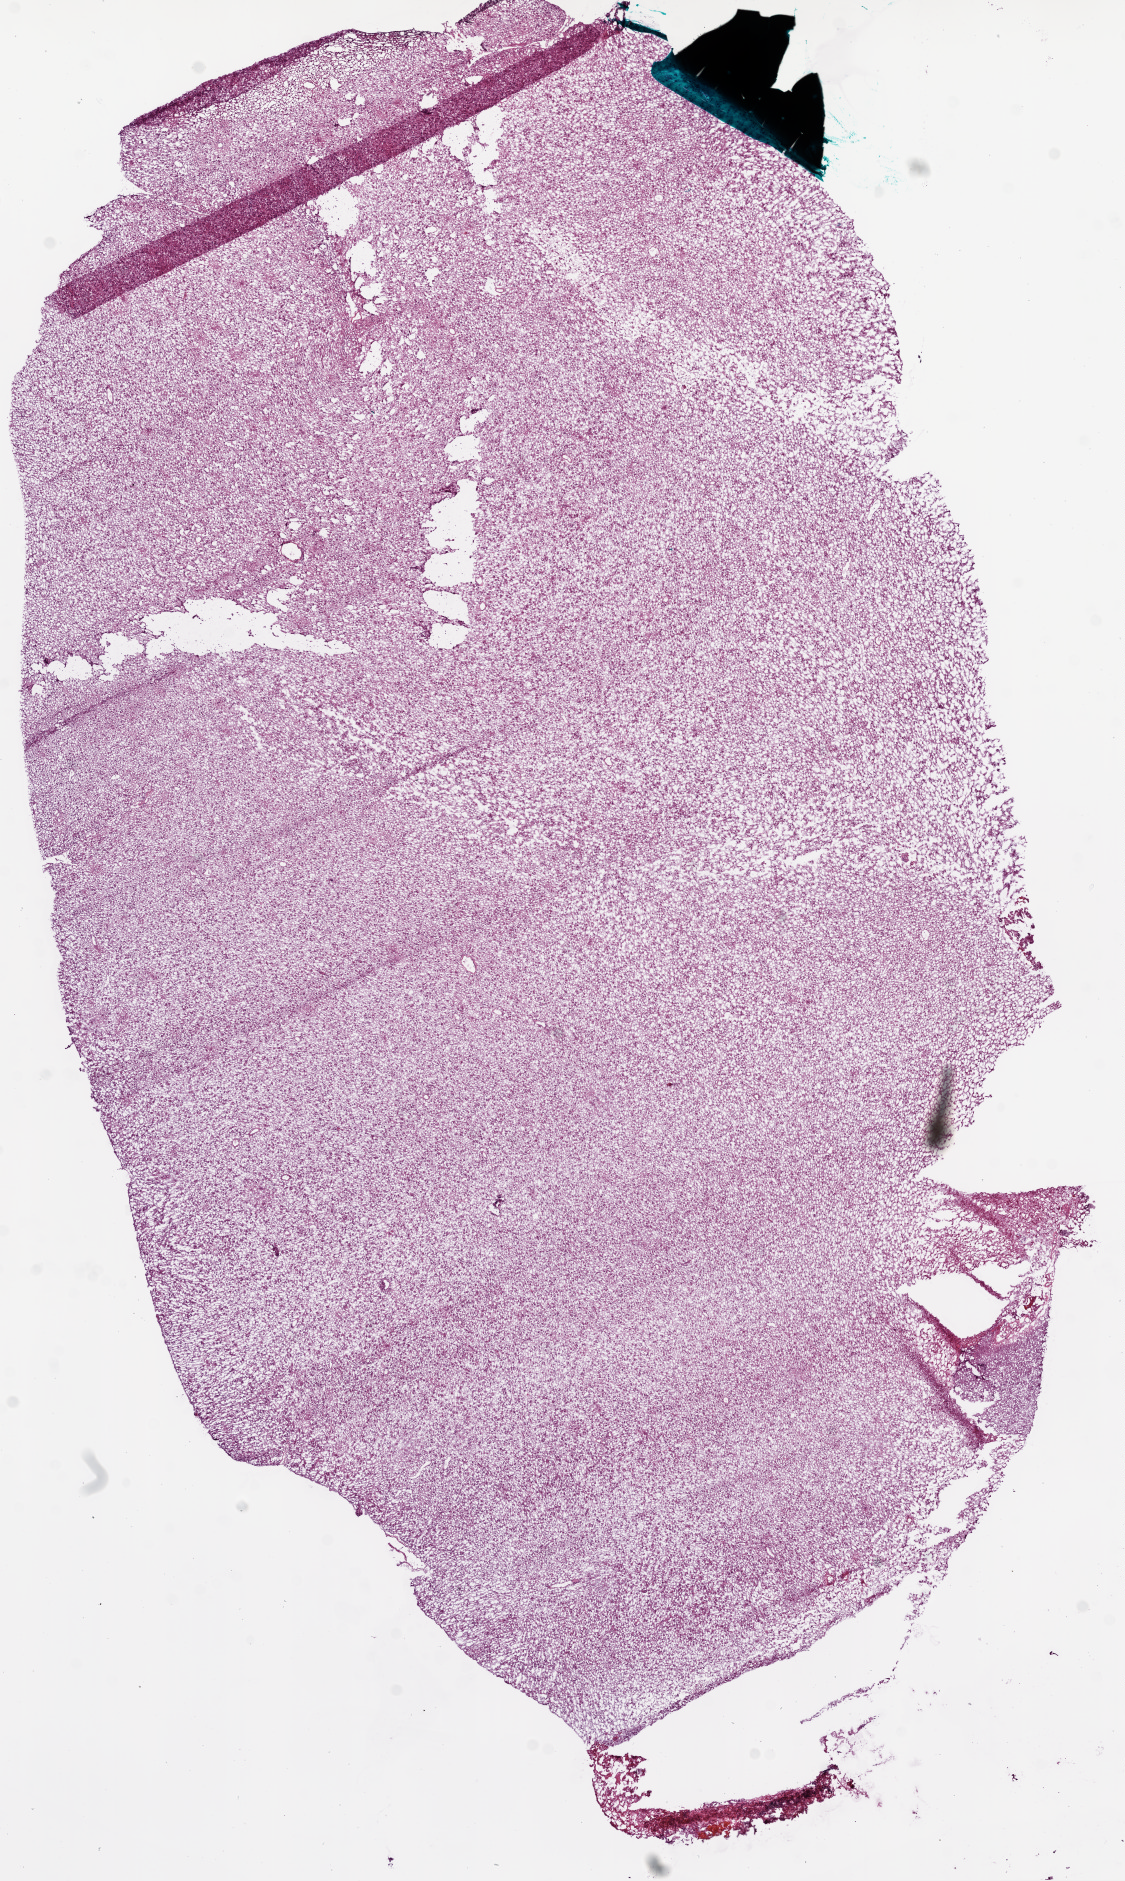
H&E whole-slide image — shown as a low-resolution overview of the whole scanned area (about 9.0 x 15.1 mm). Frozen section. Sample: primary tumour, brain. Male patient; age at initial diagnosis 55 years. Pathologist review of this section (percent, as recorded): tumour cells 95%, tumour nuclei 95%, normal cells 5%, stromal cells 0%, necrosis 0%.
Diagnosis: Glioblastoma.